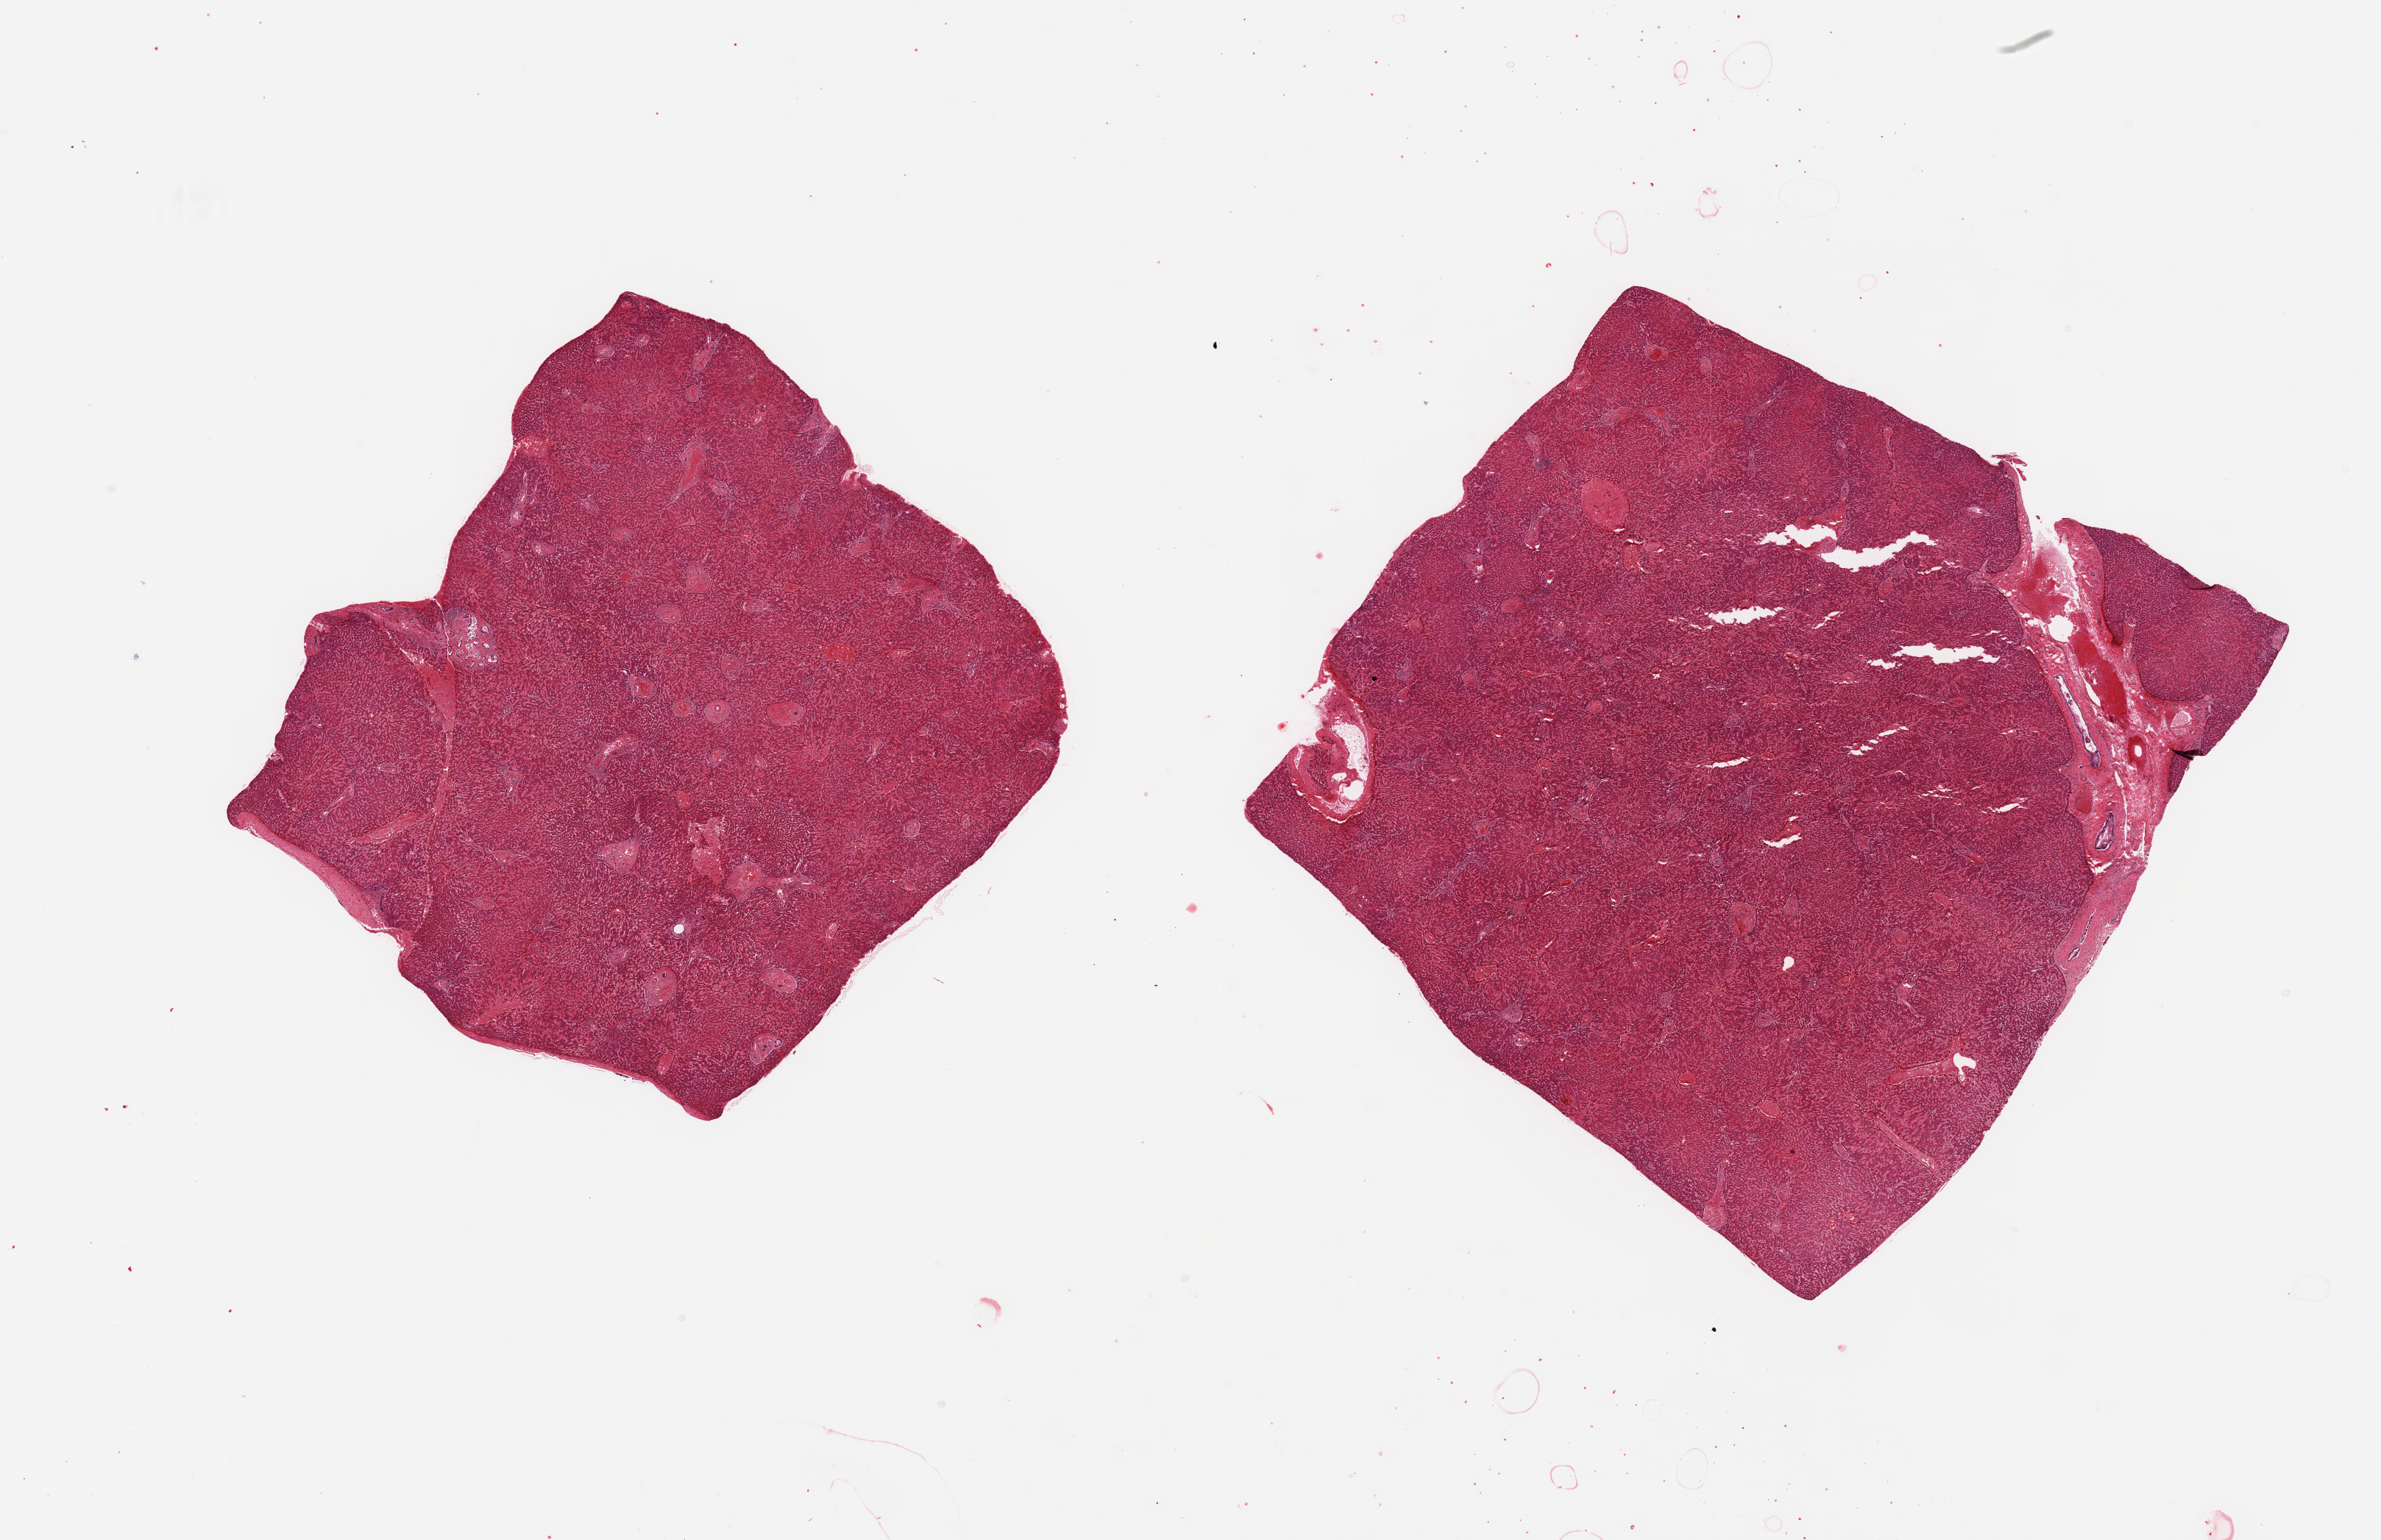
H&E whole-slide image — low-resolution overview of the scanned area, about 25.6 x 16.6 mm, PAXgene-fixed, paraffin-embedded tissue, section of liver (target tissue), tissue donor sample. Male donor.
• pathologist's review note for this sample: 2 pieces; congested, includes portion of capsule (not target region)